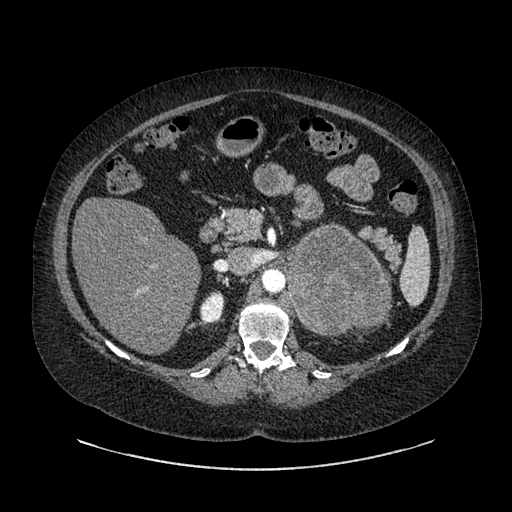
Contrast-enhanced abdominal CT, one axial slice. Position 552 of 769 along the scan axis. Intravenous contrast given. Soft-tissue window (W 400 / L 40 HU). 0.62 mm slice thickness. 512 × 512 image matrix, field of view 460 × 460 mm. Patient: female, 61 years. Case-level facts recorded for this patient, not image findings: diagnosis: adrenocortical carcinoma; tumour side: left adrenal; tumour size at pathology: 13 cm; Ki-67 index: 79 %; stage (as recorded): 2.
Outlined on this slice (semi-automatic segmentation, software-assisted and operator-edited):
- mass: bounding box (x1, y1, x2, y2) in pixels: (289, 227, 387, 335)